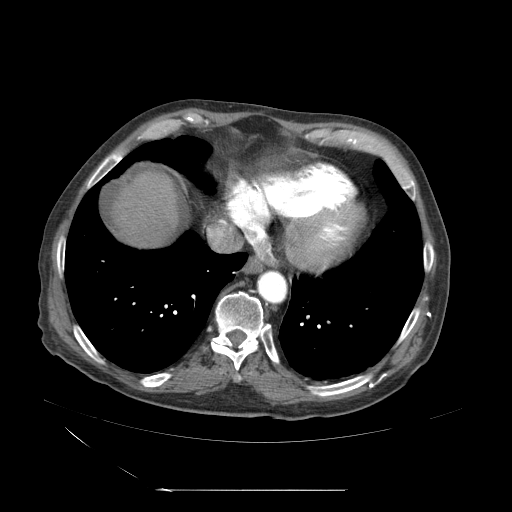
Contrast-enhanced abdominal CT (liver protocol), one axial slice. Slice 57 of 71 in the series (ordered by position). Soft-tissue window (W 400 / L 40 HU). 2.5 mm slice thickness. 512 × 512 image matrix, field of view 440 × 440 mm. From the clinical record (not read from this slice): diagnosis: hepatocellular carcinoma (patient treated with transarterial chemoembolisation; whether this scan precedes or follows treatment is not stated here); TNM stage (as recorded): Stage-II; Child-Pugh class: A.
Outlined on this slice (semi-automatic segmentation, software-assisted and operator-edited):
- abdominal aorta: box from (x=258, y=270) to (x=288, y=305) px
- liver parenchyma outside the tumour (the mass and vessels are separate outlines, so this box may not span the whole liver): (x=120, y=164)–(x=194, y=253)